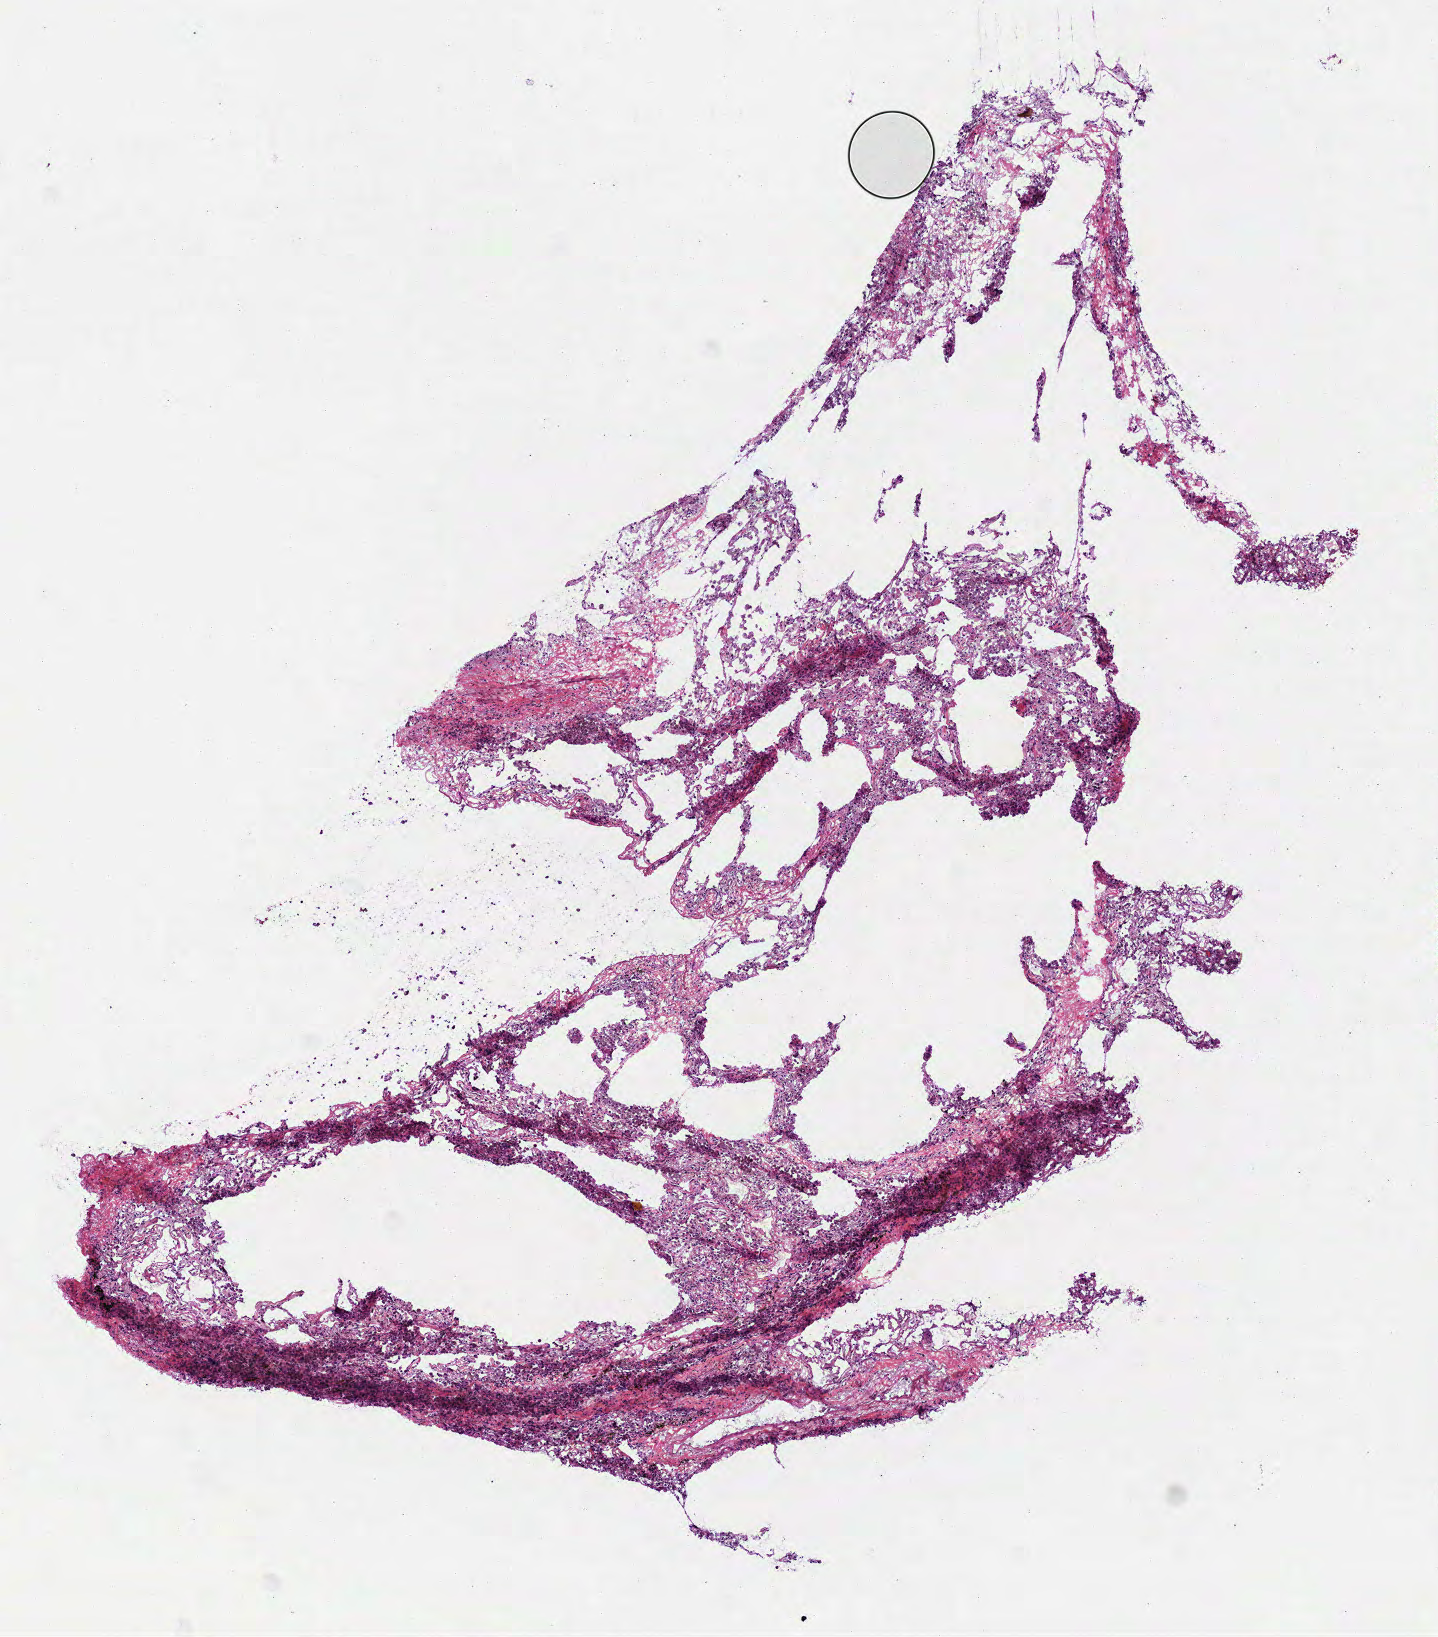
H&E whole-slide image, a low-resolution overview of the entire scanned area, about 5.8 x 6.6 mm, frozen section from the top of the tissue portion, lung, solid tissue normal (non-tumour tissue) sample. Patient: female, age at initial diagnosis 73 years.
This section: solid tissue normal (non-tumour) sample from the same patient. Patient diagnosis: Adenocarcinoma, NOS (upper lobe, lung).